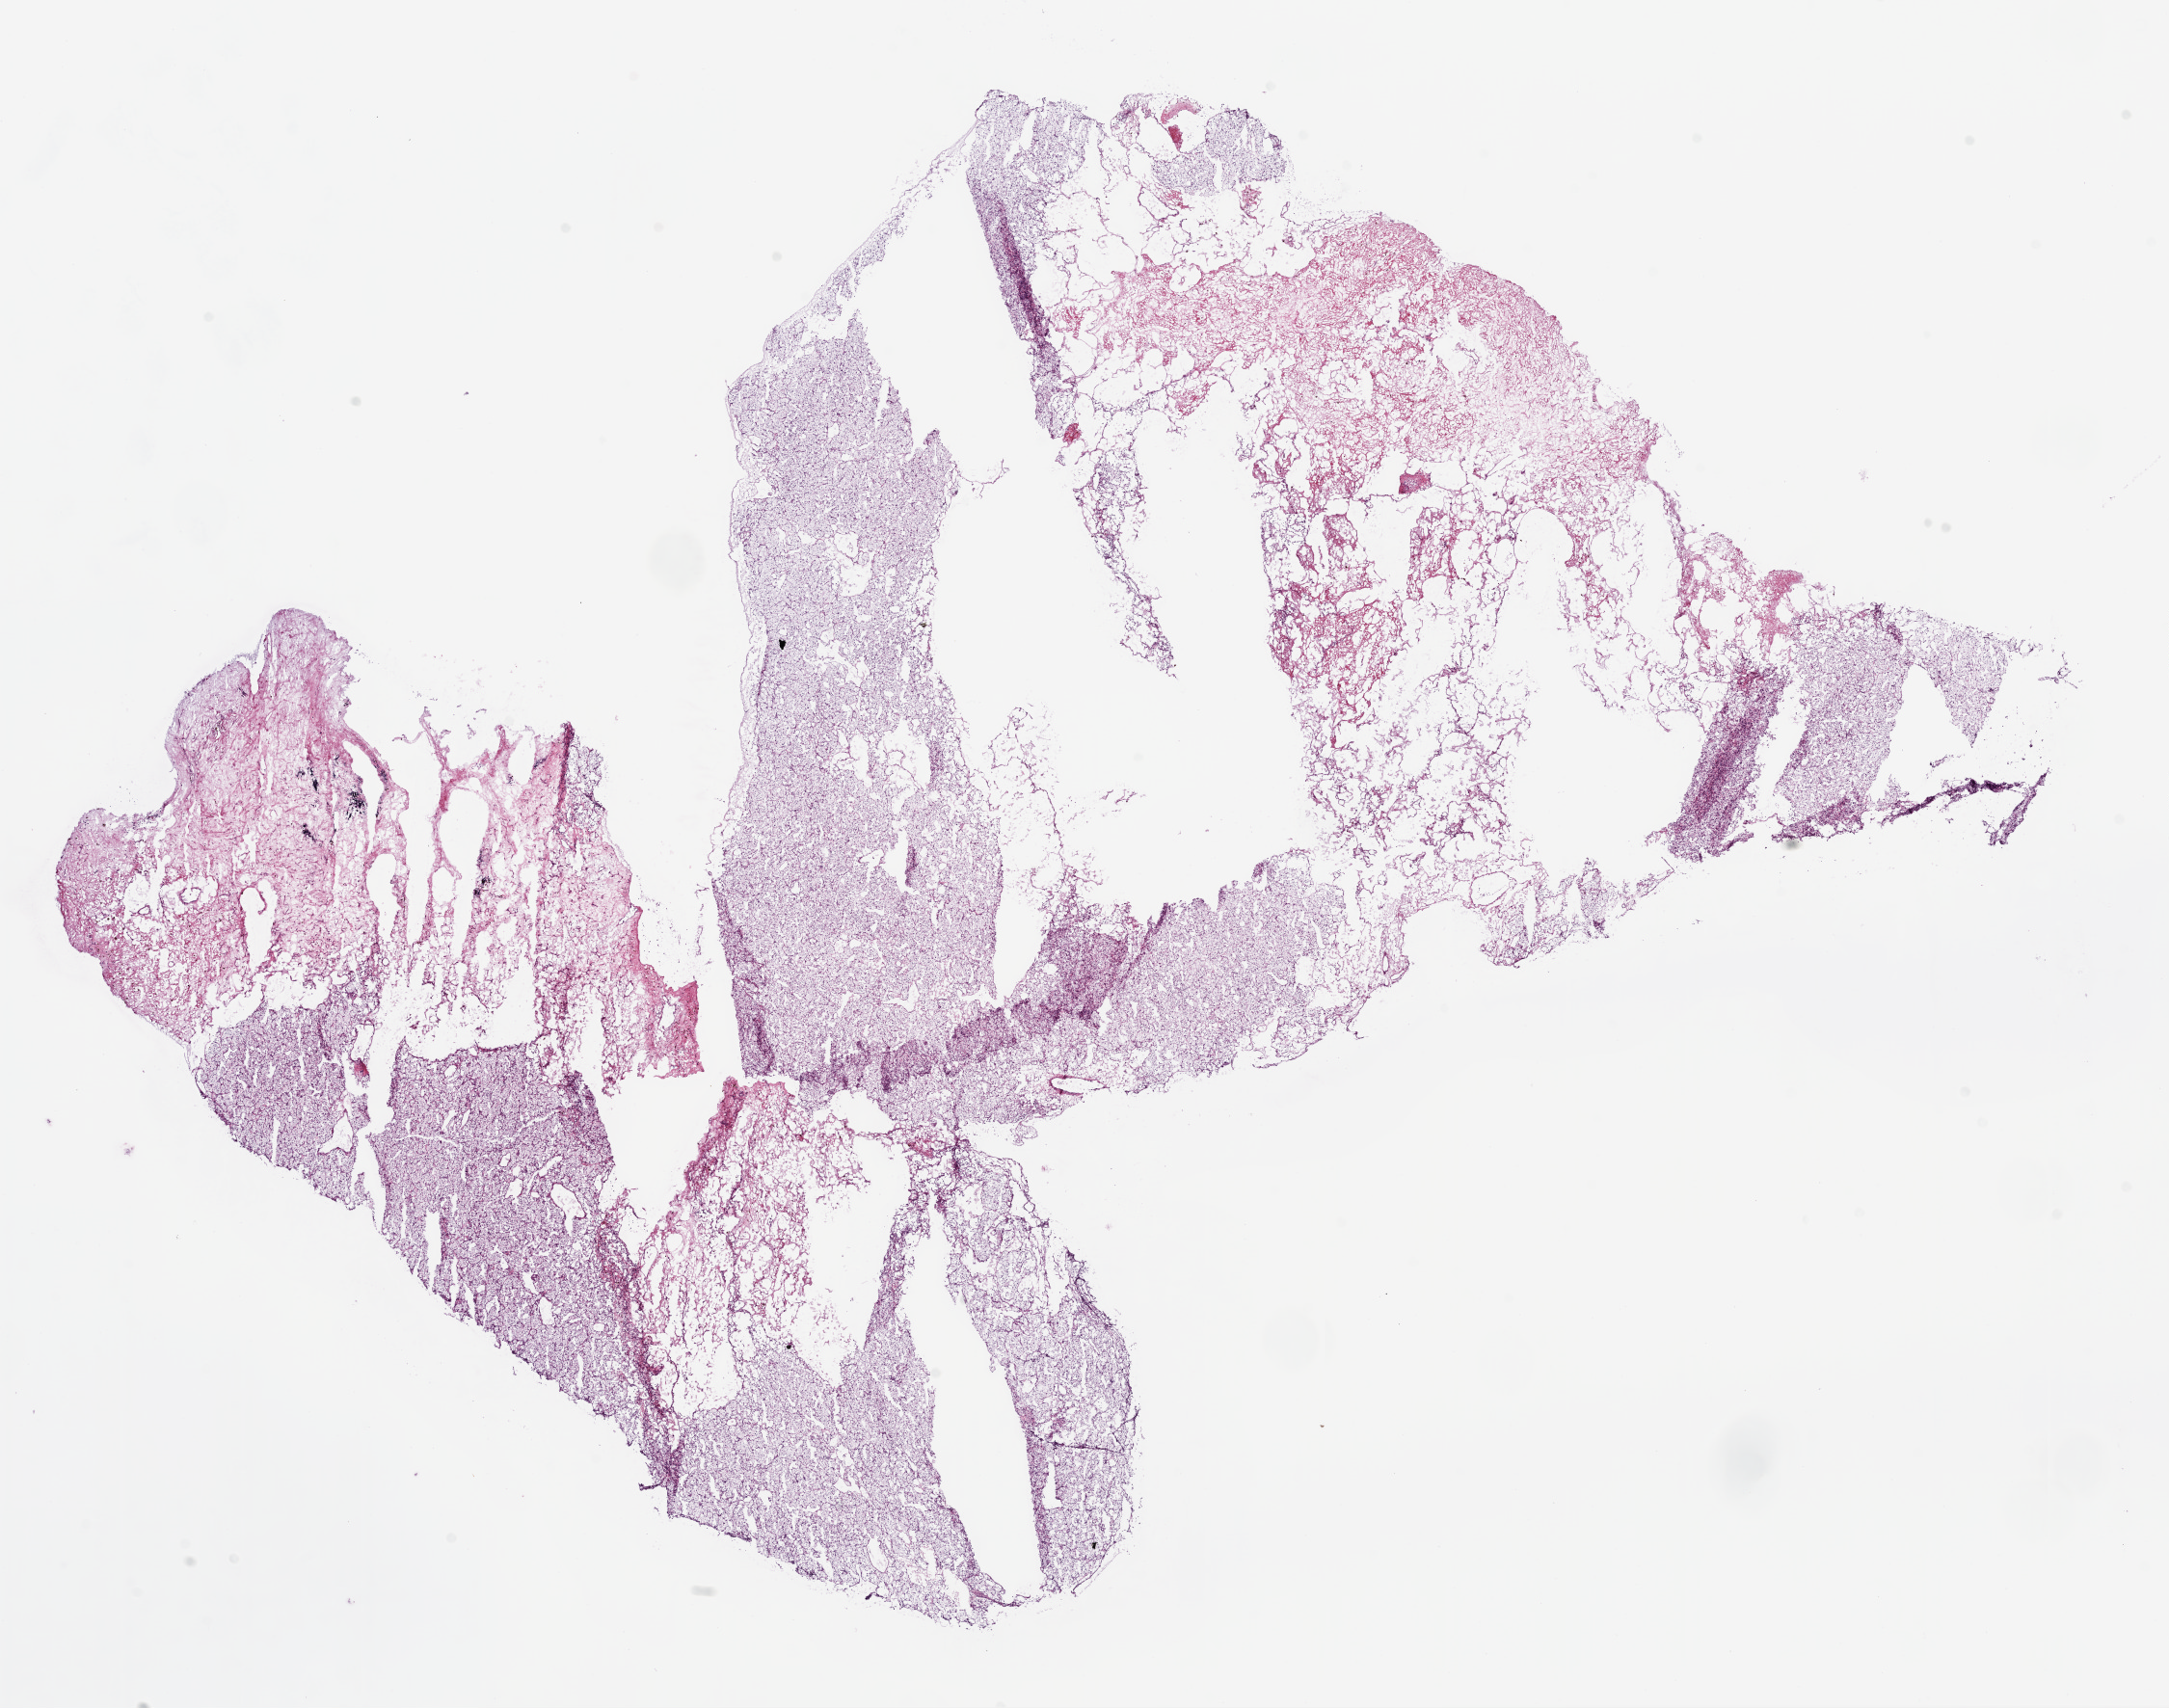
Whole-slide histology image, H&E-stained — a low-resolution overview of the entire scanned area, about 18.1 x 14.2 mm (slide scanned at 20x); frozen section from the bottom of the tissue portion; primary tumour sample from the kidney. Male, age 39 years at initial diagnosis. Histologic grade: G2 (moderately differentiated). Pathologist review of this section (percent, as recorded): tumour cells 75%, tumour nuclei 85%, normal cells 0%, stromal cells 25%, necrosis 0%.
• histologic diagnosis: Clear cell adenocarcinoma, NOS
• AJCC pathologic stage: I
• laterality: right